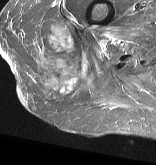
MRI of an extremity soft-tissue mass, one axial slice; slice 15 of 57 in the series (ordered by position); STIR; MR volume resampled by the dataset authors to the PET/CT grid (not the native acquisition matrix); 3.27 mm slice thickness; 156 × 165 image matrix, field of view 152 × 161 mm. Female patient. From the clinical record (not read from this slice): histological type: epithelioid sarcoma with vascular differentiation; site of the primary tumour: right buttock.
Structures marked on this image (expert contour drawn on MRI and transferred to this co-registered scan by the dataset authors):
- gross tumour volume (mass): bounding box [x1, y1, x2, y2] px = [35, 26, 96, 100]